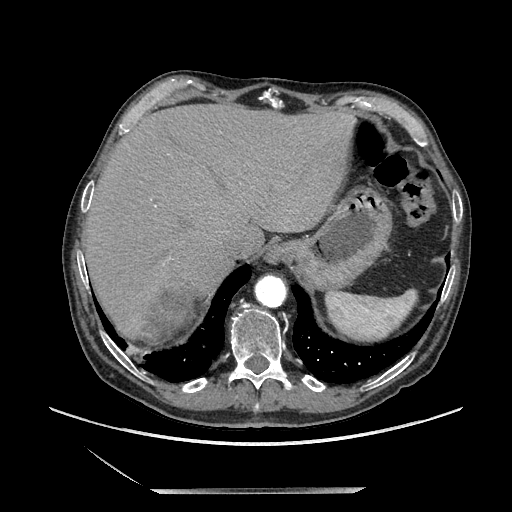
Contrast-enhanced abdominal CT, one axial slice; soft-tissue window (W 400 / L 40 HU); 1.25 mm slice thickness; 512 × 512 image matrix. Male patient. Case-level facts recorded for this patient, not image findings: diagnosis: adrenocortical carcinoma; tumour side: right adrenal; tumour size at pathology: 16 cm; Ki-67 index: 17 %; stage (as recorded): 3.
Annotated regions visible in this slice (semi-automatic segmentation, software-assisted and operator-edited):
- mass: box from (x=138, y=293) to (x=195, y=346) px